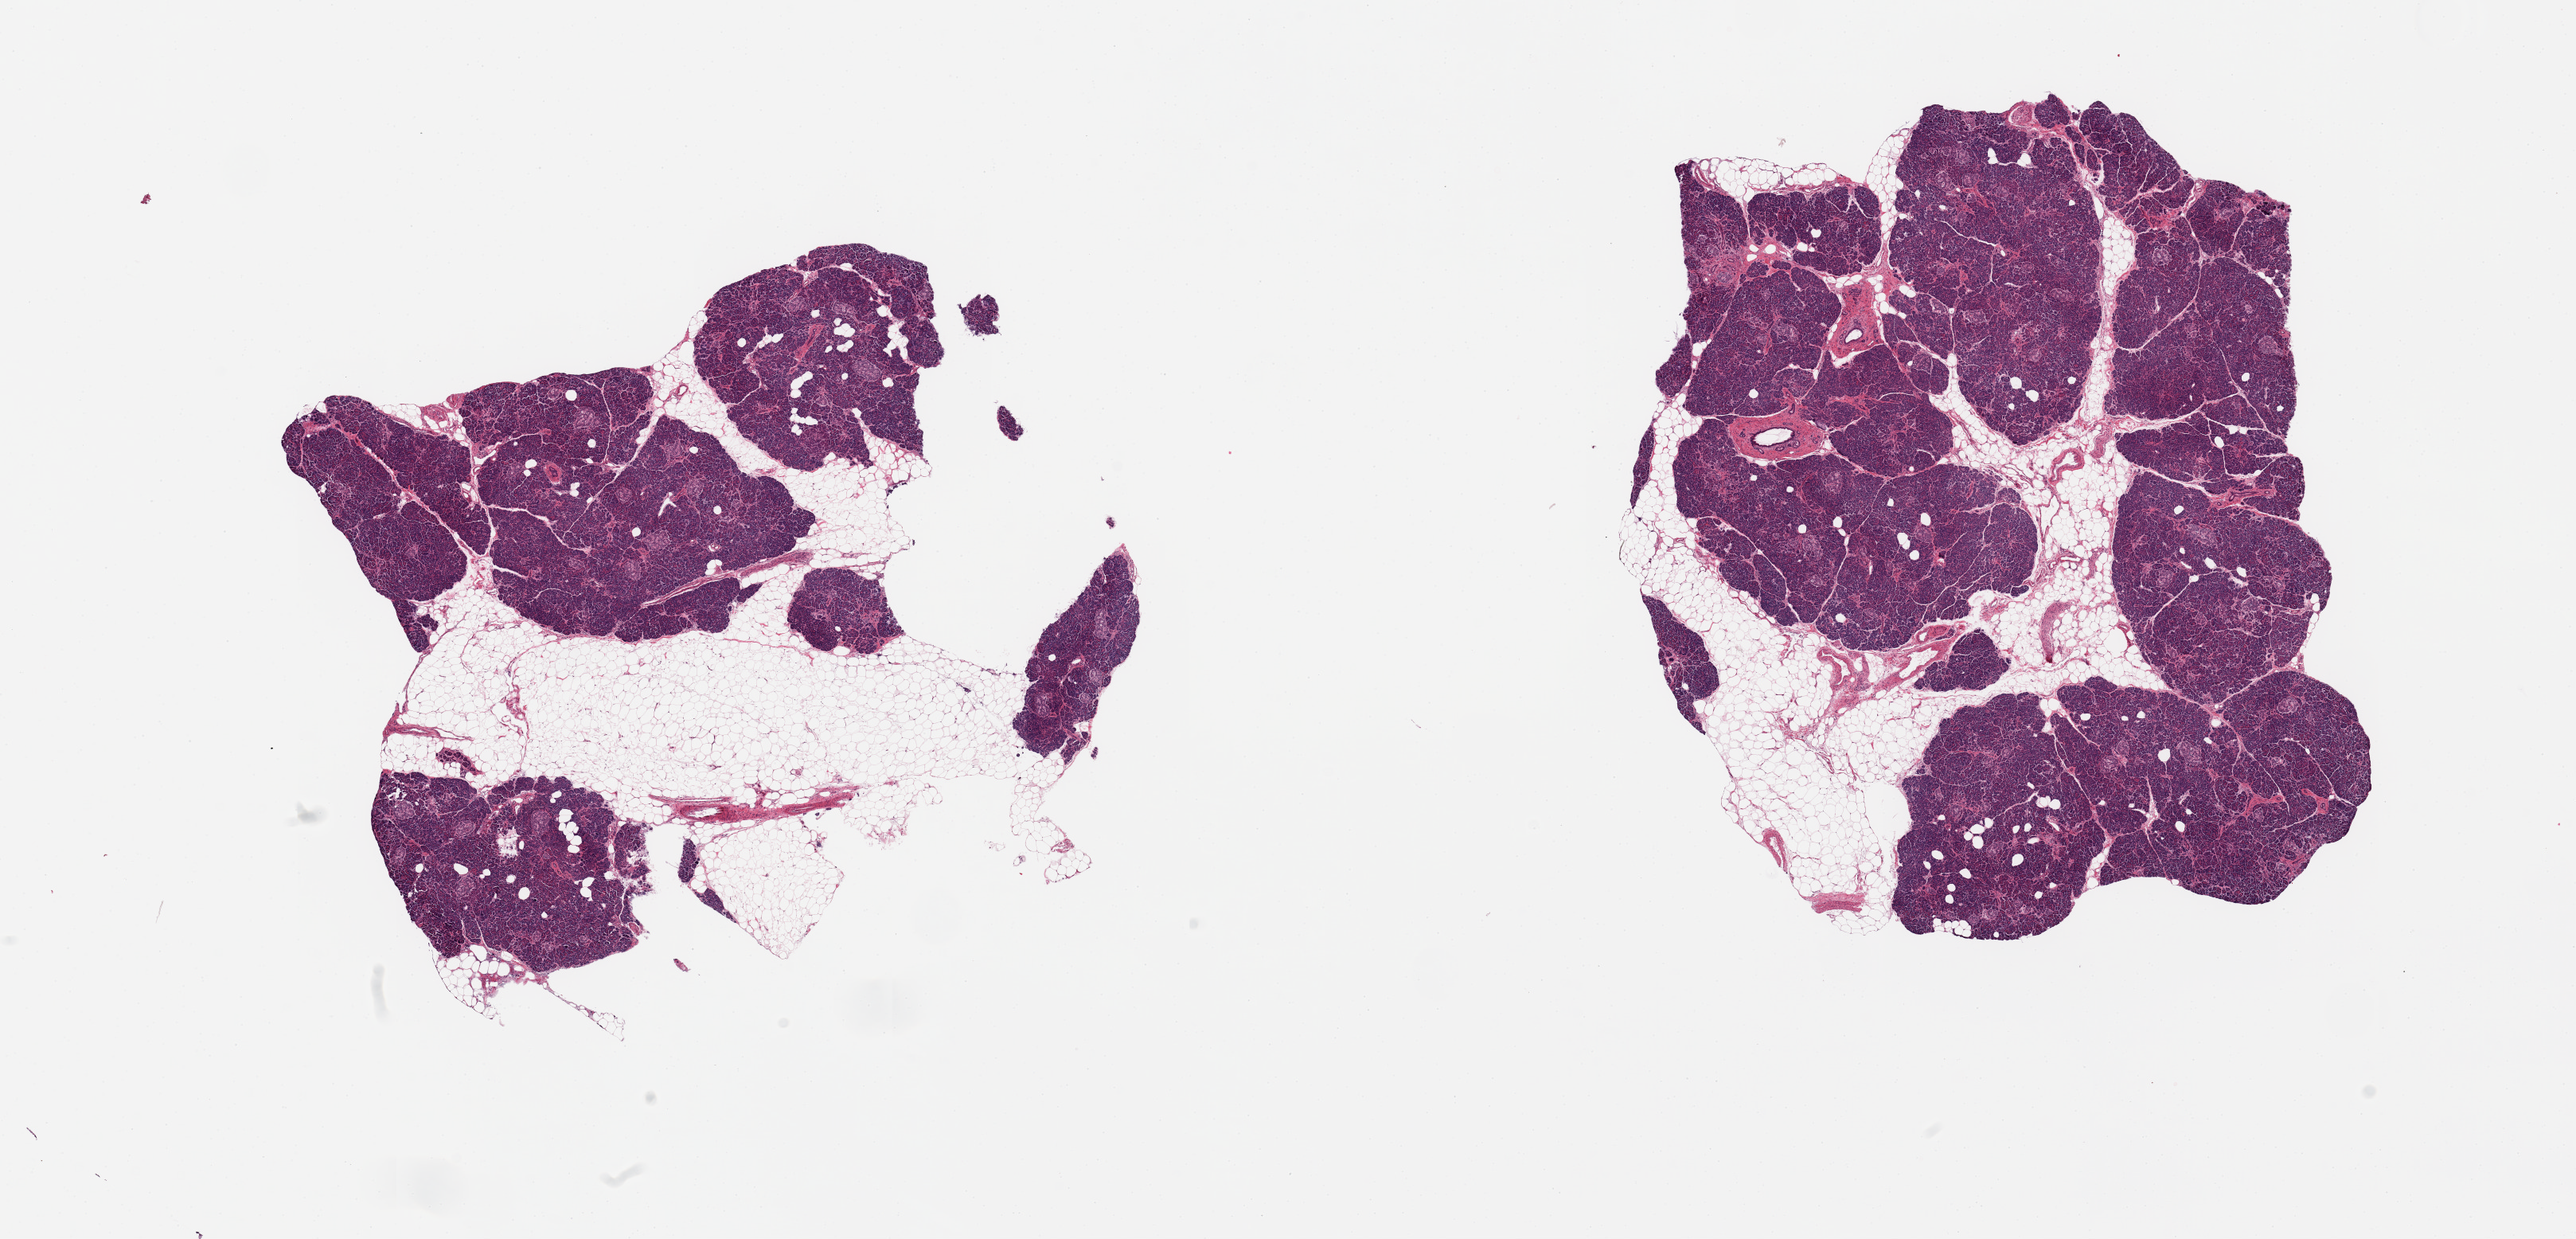
Whole-slide image, H&E stain, whole scanned area (about 25.6 x 12.3 mm) shown as a low-resolution overview. PAXgene-fixed, paraffin-embedded tissue. Target tissue: pancreas. Tissue donor sample. Donor: female.
Review note (as recorded): 2 pieces; 20 and 40% fat, islets well visualized, mild fibrosis.